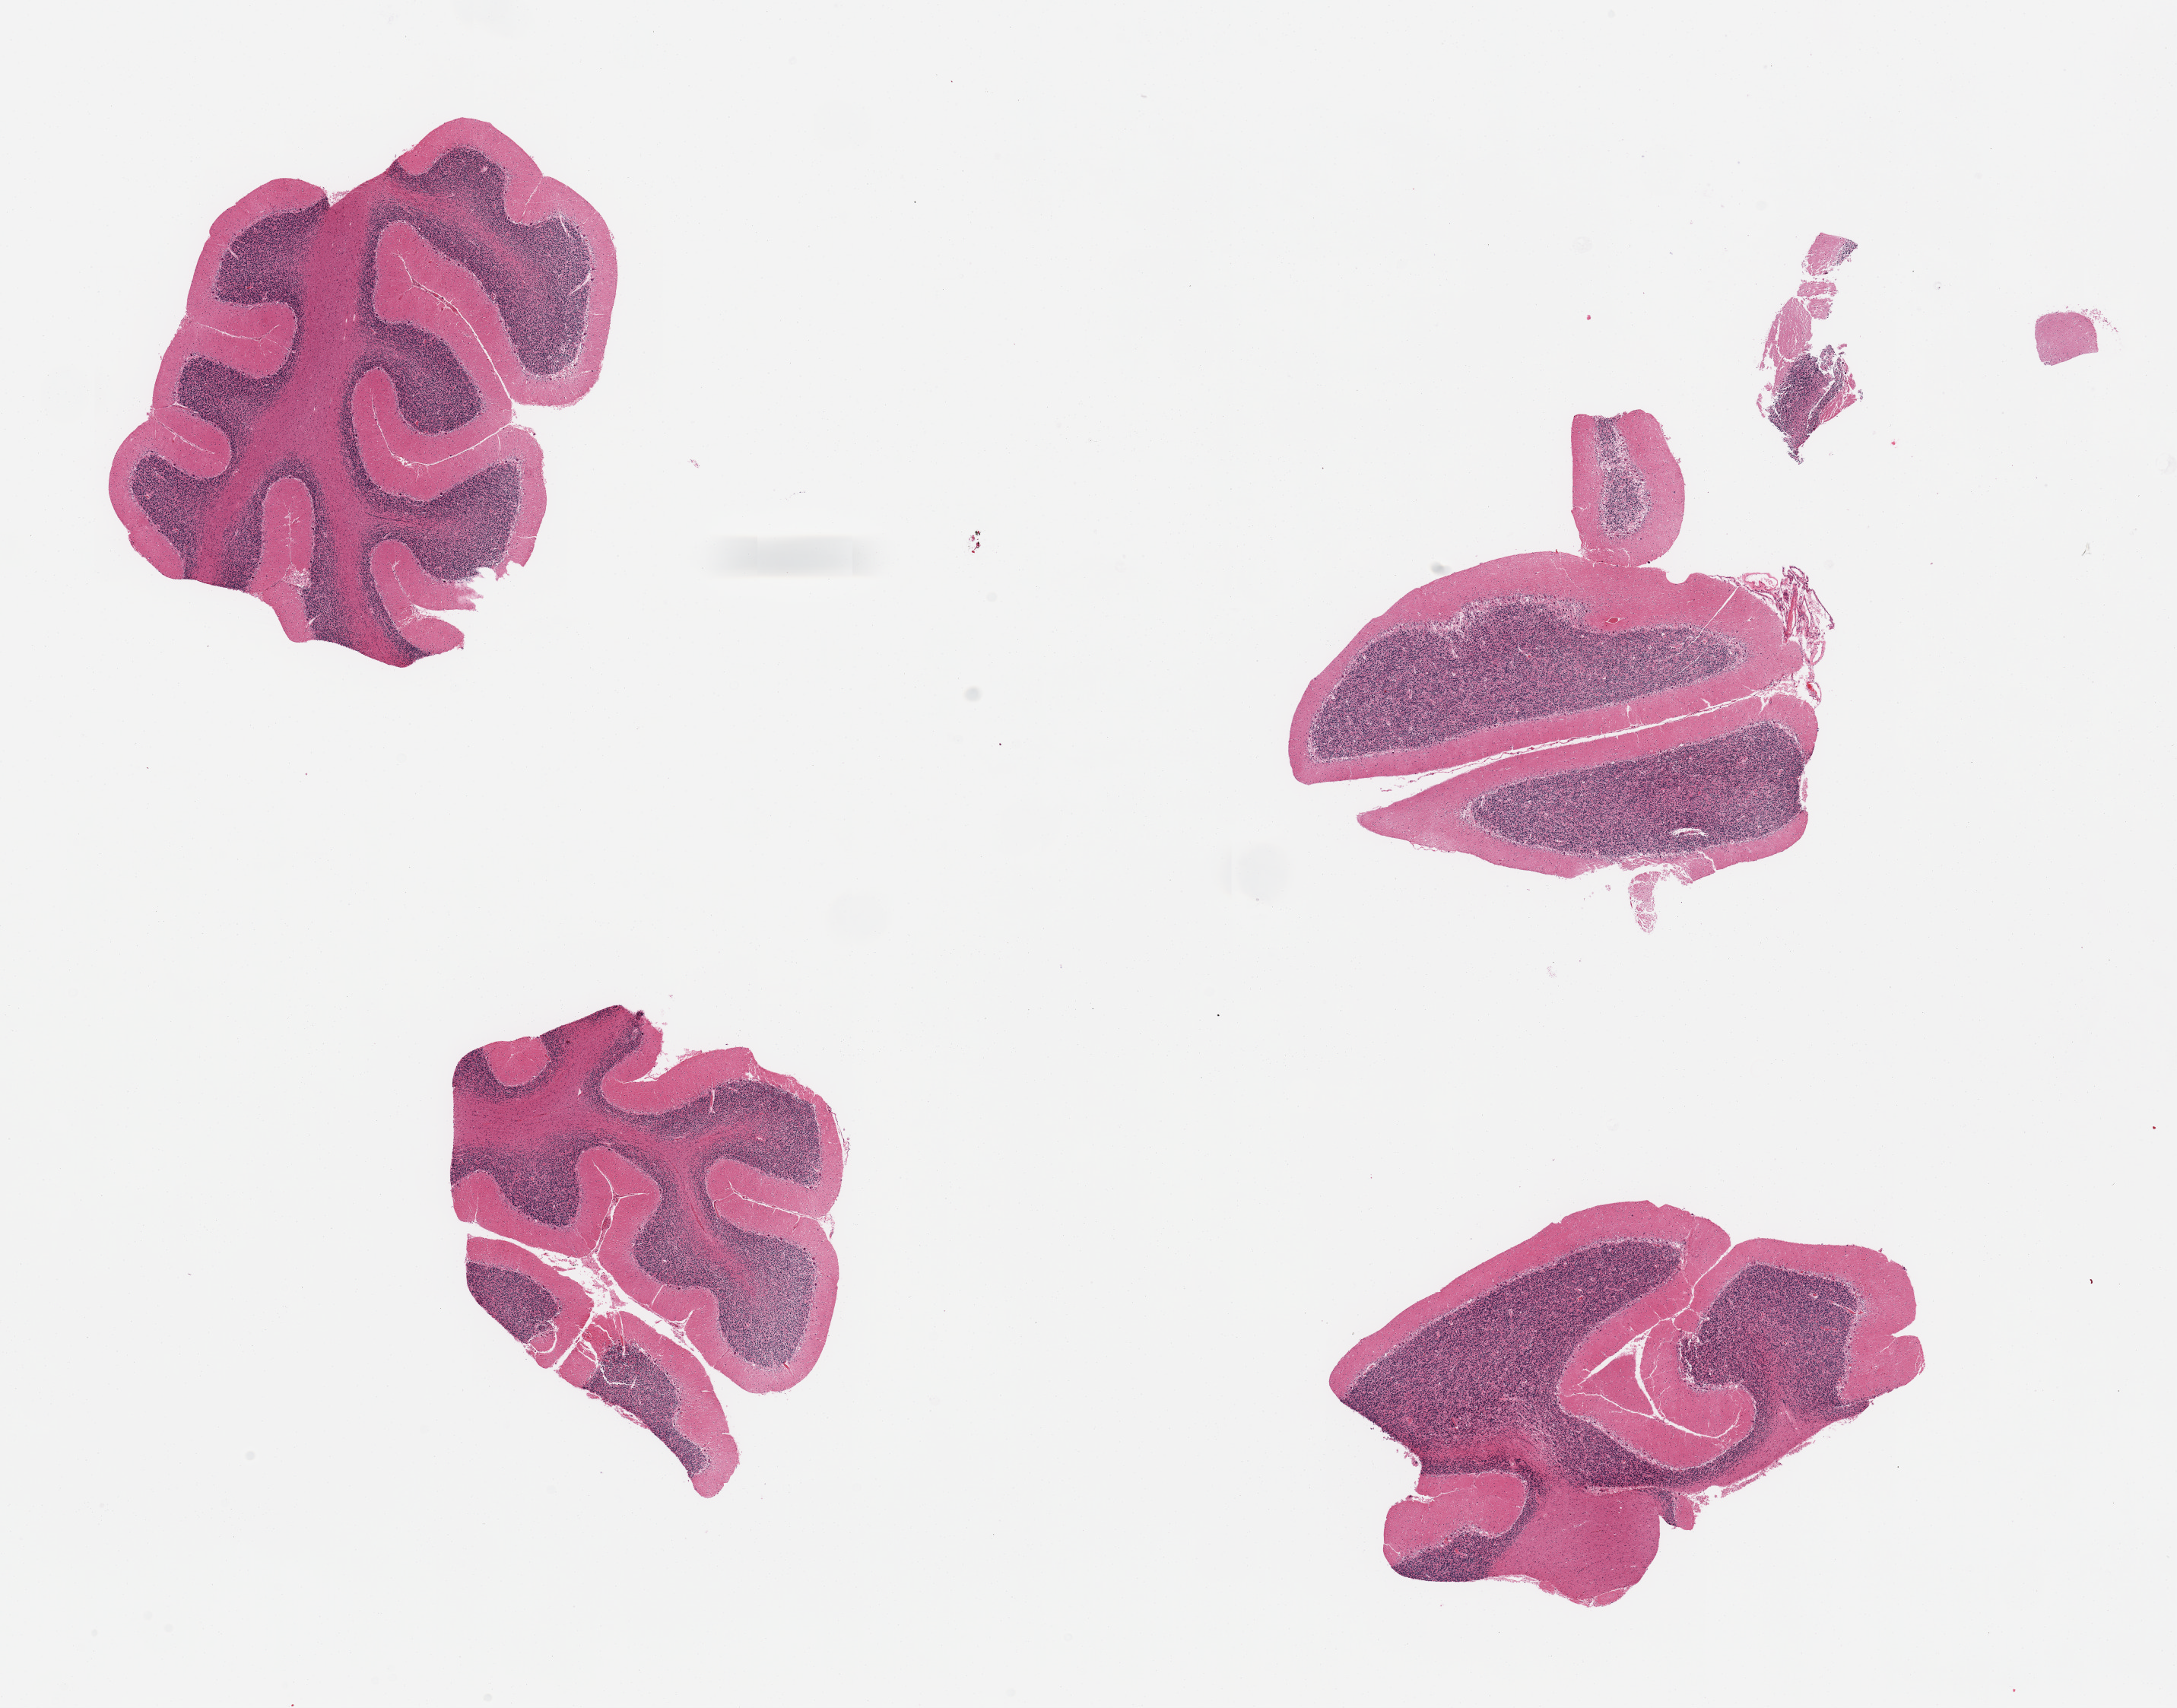
Haematoxylin and eosin whole-slide image, shown as a low-resolution overview of the whole scanned area (about 22.6 x 17.8 mm), PAXgene-fixed paraffin-embedded (PFPE) section, section of cerebellum (target tissue), donor tissue sample. Male donor.
Pathologist's review note for this sample: 4 pieces, no abnormalities.